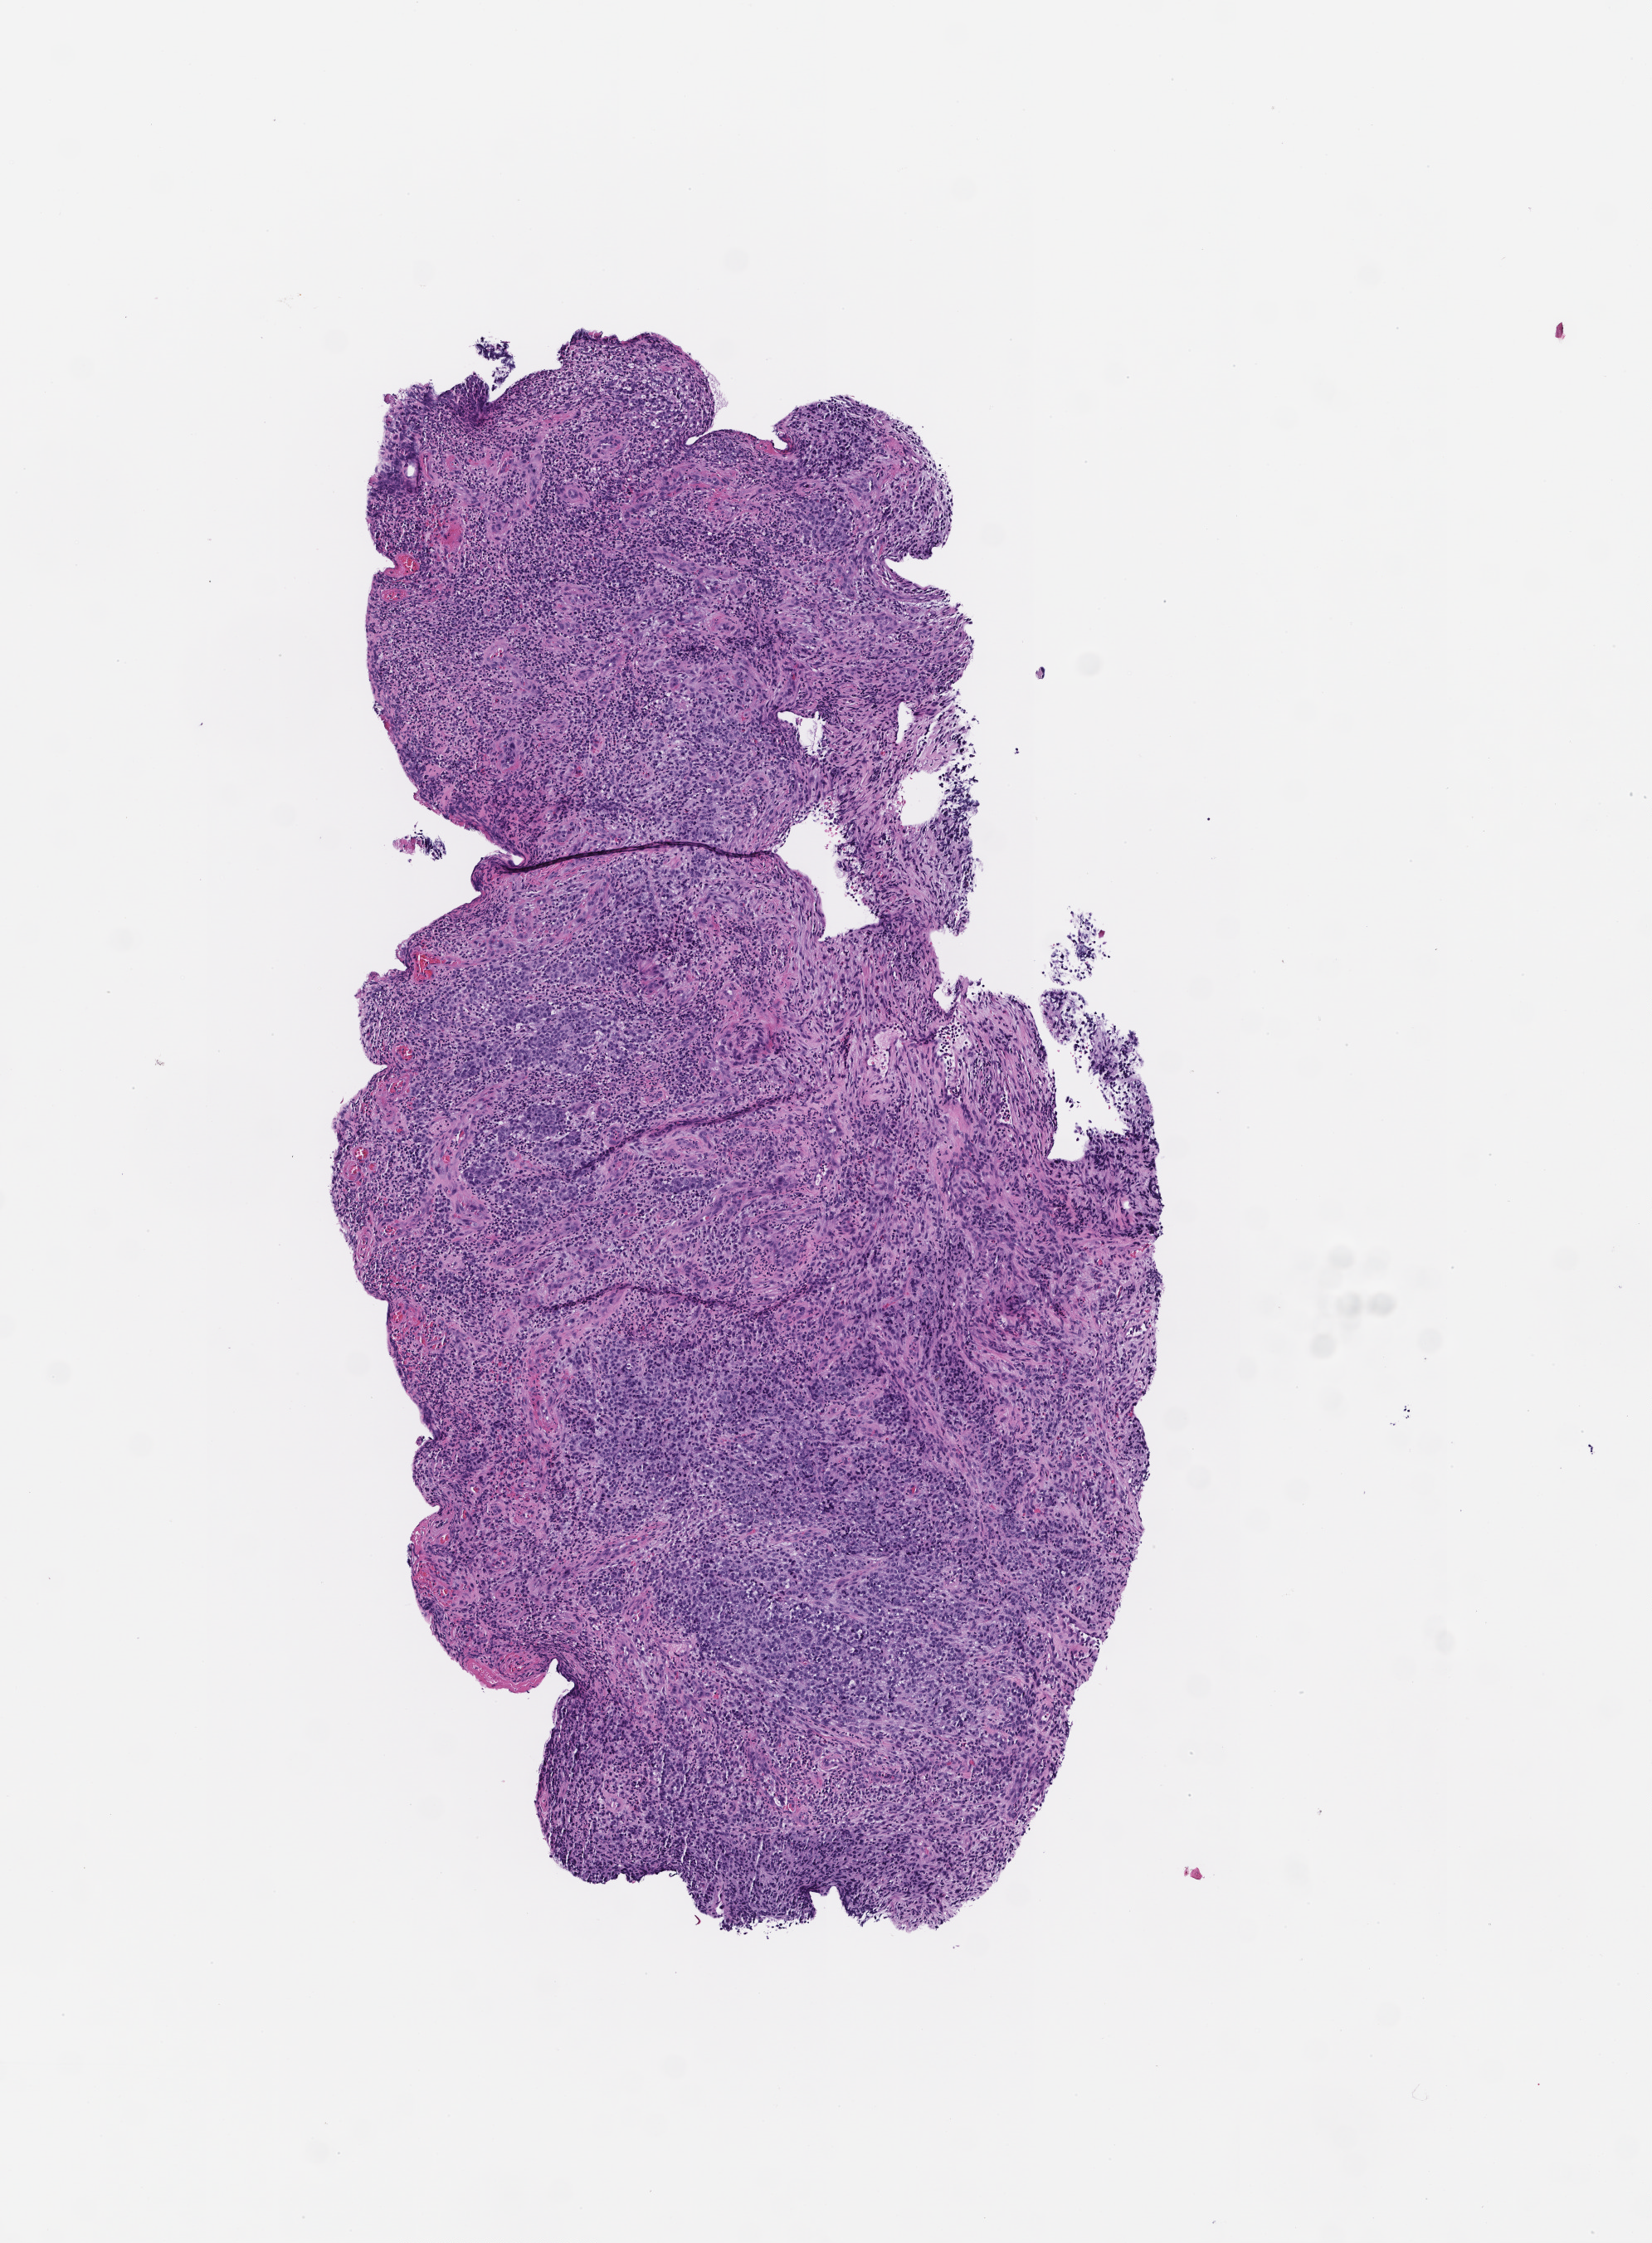
Hematoxylin and eosin (H&E) whole-slide image, low-resolution overview of the scanned area, about 4.0 x 5.5 mm, formalin-fixed, paraffin-embedded (FFPE) tissue, site: skin, specimen time point: collected at baseline (before treatment). Patient sex: female.
This section: primary tumour tissue. Diagnosis: Melanoma.